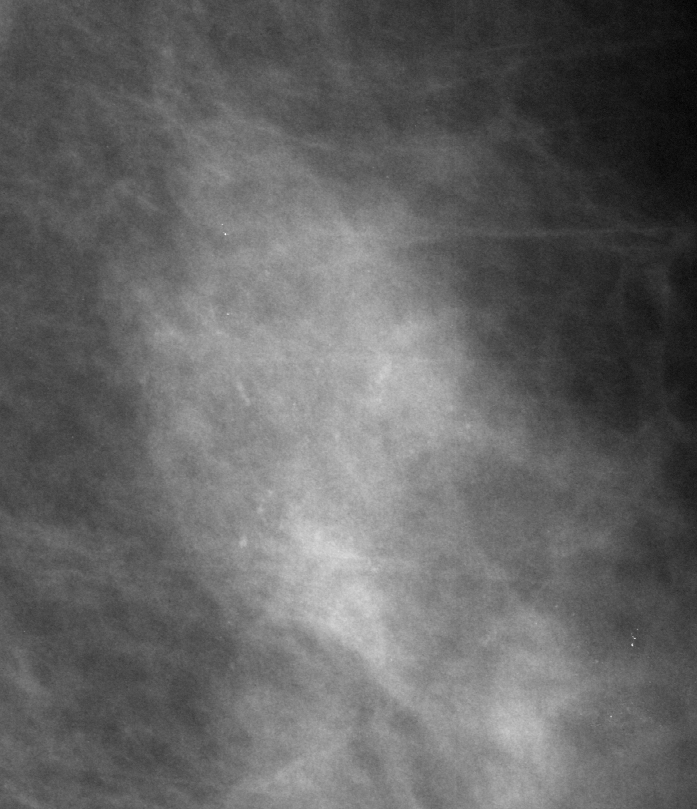
Region of interest cut from a scanned film mammogram (one marked finding); left breast; MLO view.
Calcifications, morphology punctate, distribution segmental; BI-RADS assessment category 4; subtlety rating 3 on a 1 (subtle) to 5 (obvious) scale; pathology (as recorded): benign.